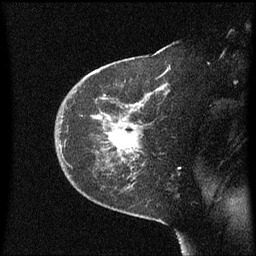
Breast MRI (dynamic contrast-enhanced), one sagittal slice. Position 43 of 60 along the scan axis. Dynamic contrast-enhanced series, image 2 of 3 at this slice position (ordered by acquisition). 1.5 T. TE 4.2 ms, TR 8.4 ms. 2 mm slice thickness. 256 × 256 image matrix, field of view 200 × 200 mm. Patient: female, 38 years. Case-level facts recorded for this patient, not image findings: setting: breast cancer imaged before/during neoadjuvant chemotherapy; receptor status: HER2-positive.
Annotated regions visible in this slice (semi-automatic segmentation, software-assisted and operator-edited):
- analysis volume of interest (the breast-tissue region the enhancement analysis was run in; not a lesion): bounding box <55,50,171,185> (left, top, right, bottom; pixels)
- tumour enhancement mask (voxels above the 70 % enhancement threshold inside the analysis volume of interest): <127,110,133,153>